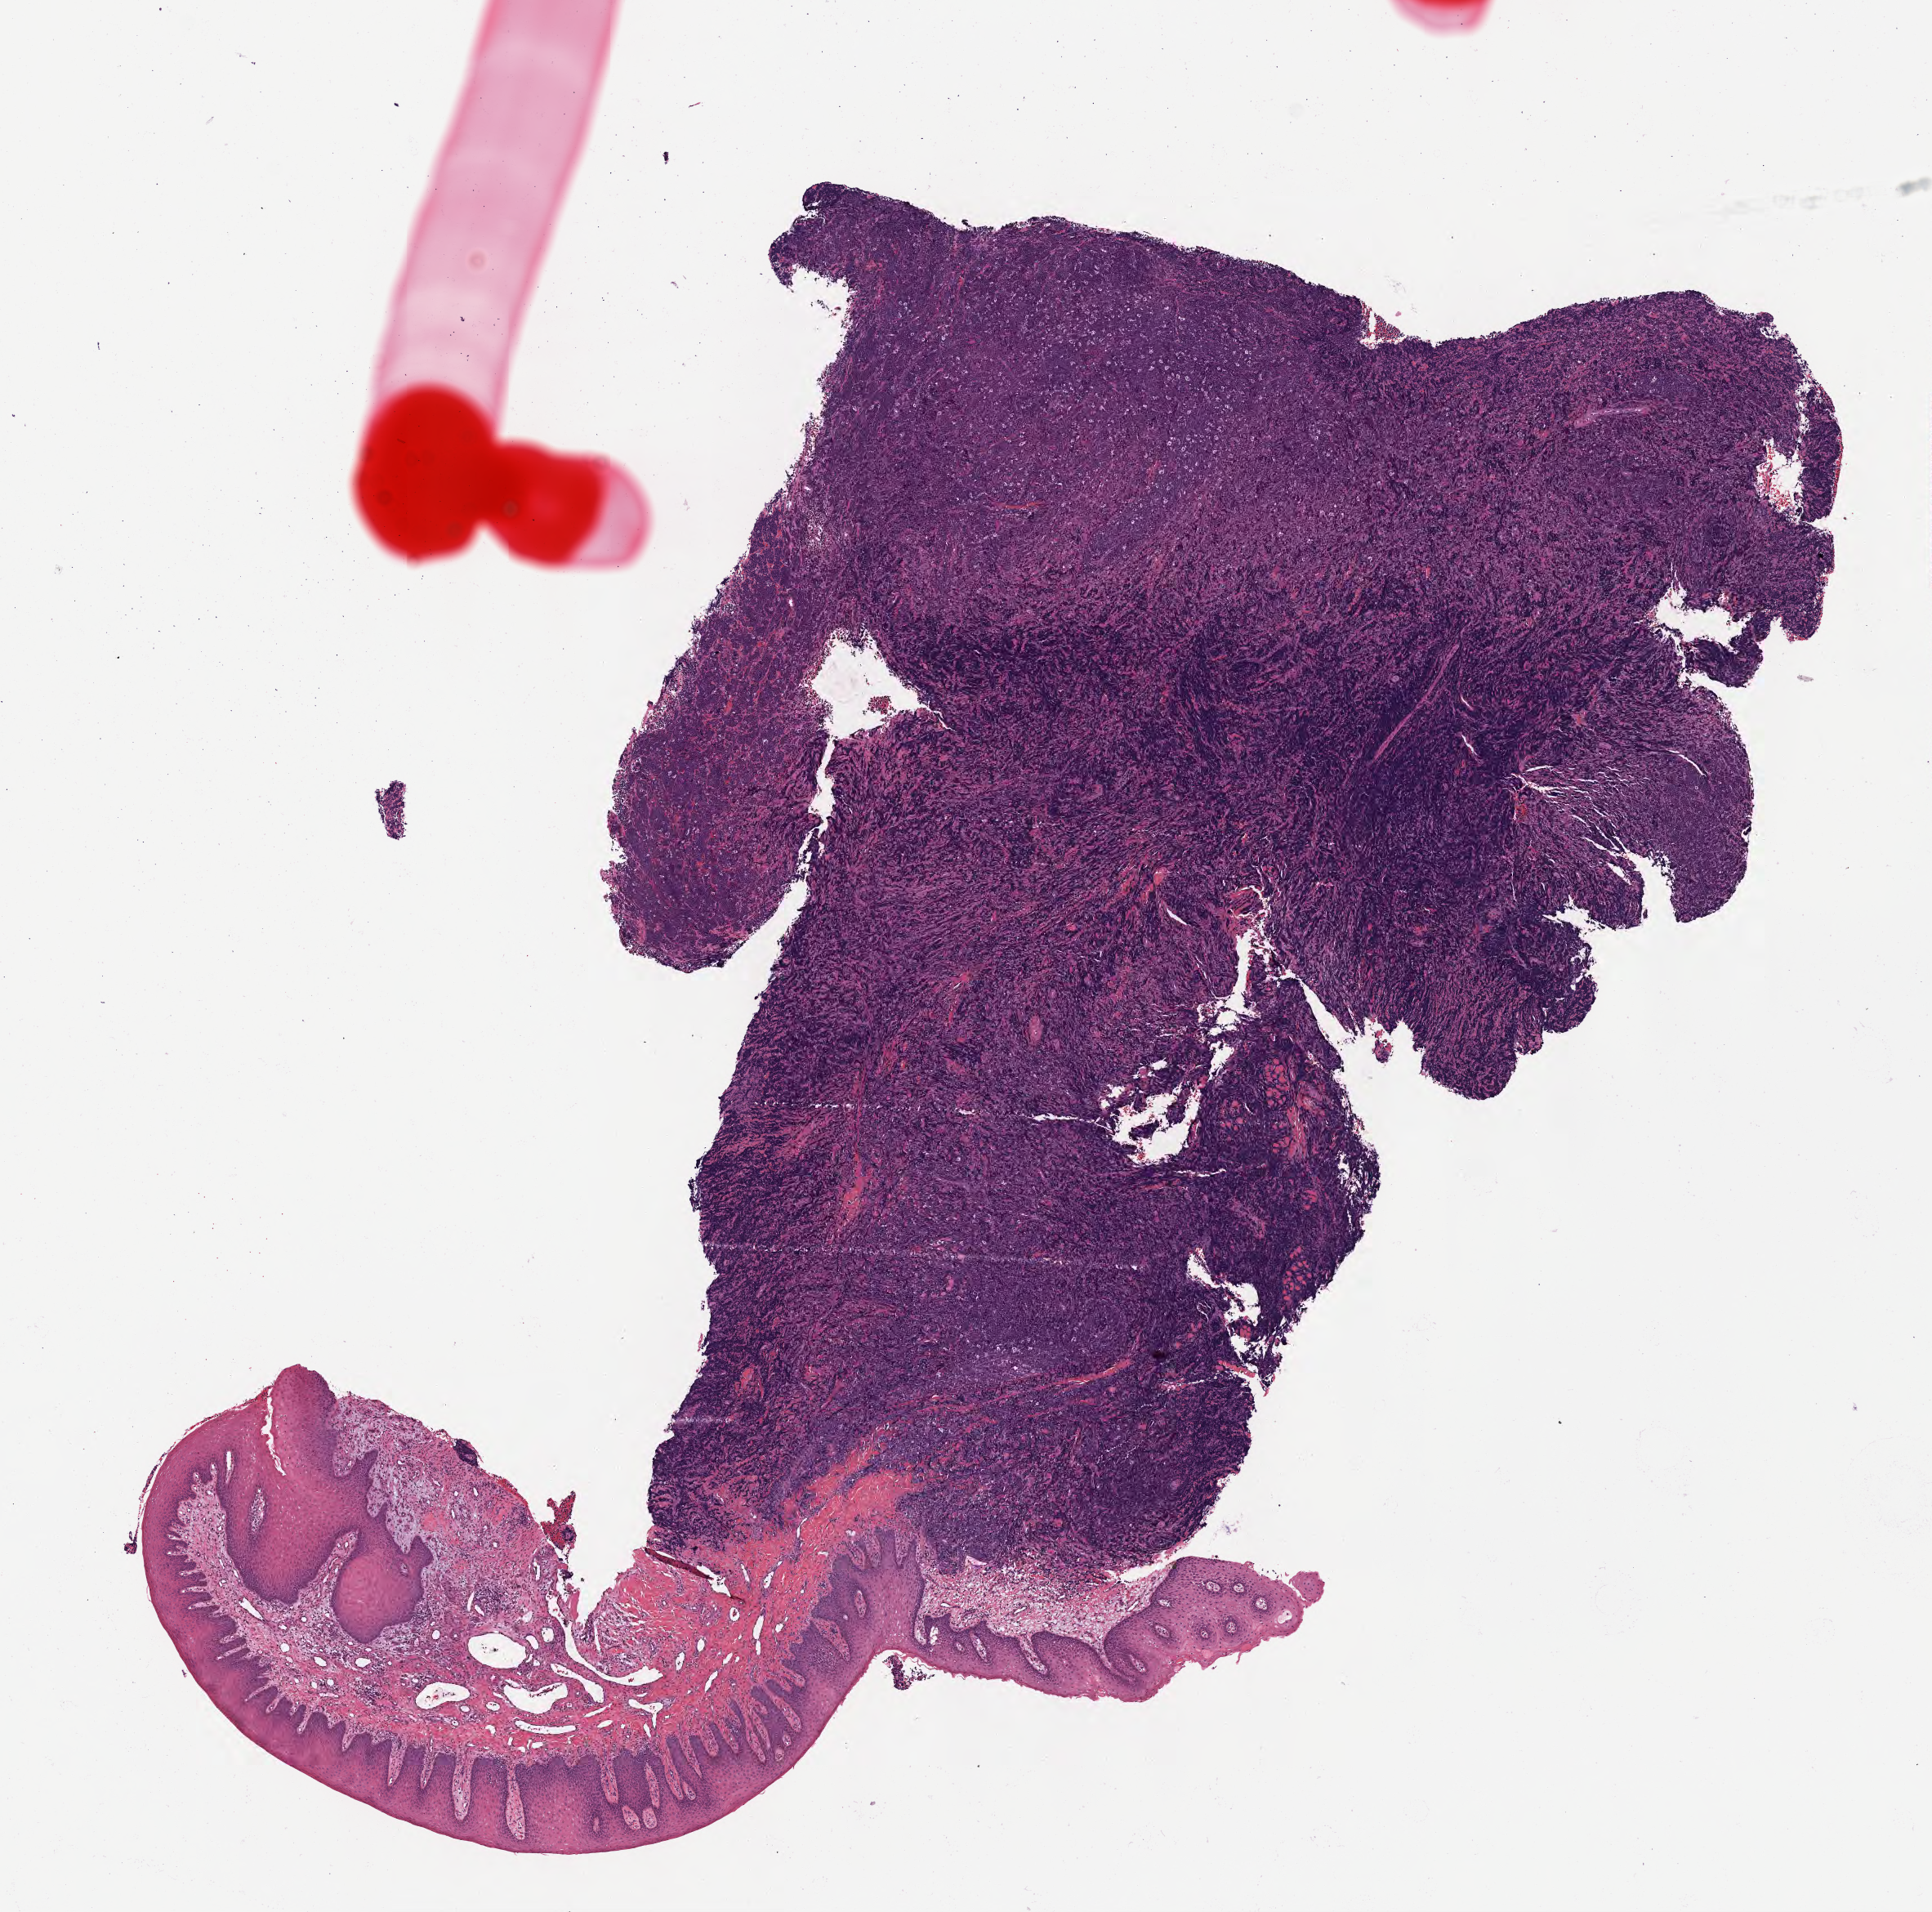
H&E whole-slide image, a low-resolution overview of the entire scanned area, about 9.6 x 9.5 mm; formalin-fixed, paraffin-embedded (FFPE) tissue; primary tumor; site: cranium. Female patient; age at initial diagnosis 6 years. Pathologist review of this section (percent, as recorded): tumor cells 80%, tumor nuclei 90%, stromal cells 10%, necrosis 0%, normal cells 10%. Inflammatory infiltration, as recorded: lymphocyte infiltration 40%, monocyte infiltration 30%, neutrophil infiltration 5%.
Ann Arbor stage (patient): Stage III. Section: top of the tissue portion. Diagnosis: Burkitt lymphoma, NOS.